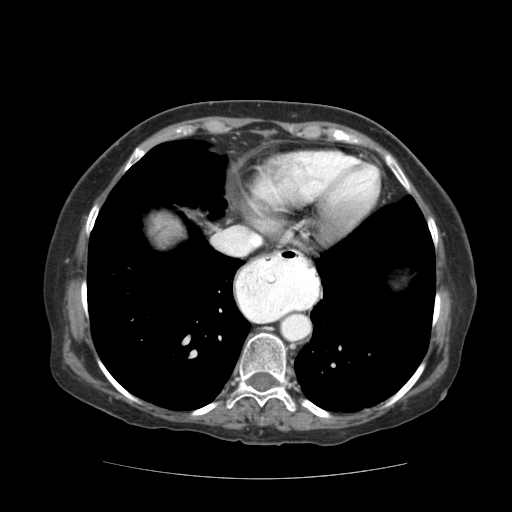
Contrast-enhanced abdominal CT (liver protocol), one axial slice. Position 98 of 111 along the scan axis. Reconstruction kernel STANDARD. Soft-tissue window (W 400 / L 40 HU). 512 × 512 image matrix. From the clinical record (not read from this slice): diagnosis: hepatocellular carcinoma (patient treated with transarterial chemoembolisation; whether this scan precedes or follows treatment is not stated here); TNM stage (as recorded): Stage-I; Child-Pugh class: A; tumour nodularity: uninodular; tumour size: 7.3 cm.
Structures marked on this image (semi-automatic segmentation, software-assisted and operator-edited):
- abdominal aorta: bounding box [x1, y1, x2, y2] px = [282, 314, 309, 340]
- liver parenchyma outside the tumour (the mass and vessels are separate outlines, so this box may not span the whole liver): [151, 220, 184, 246]
- mass: [151, 214, 181, 243]